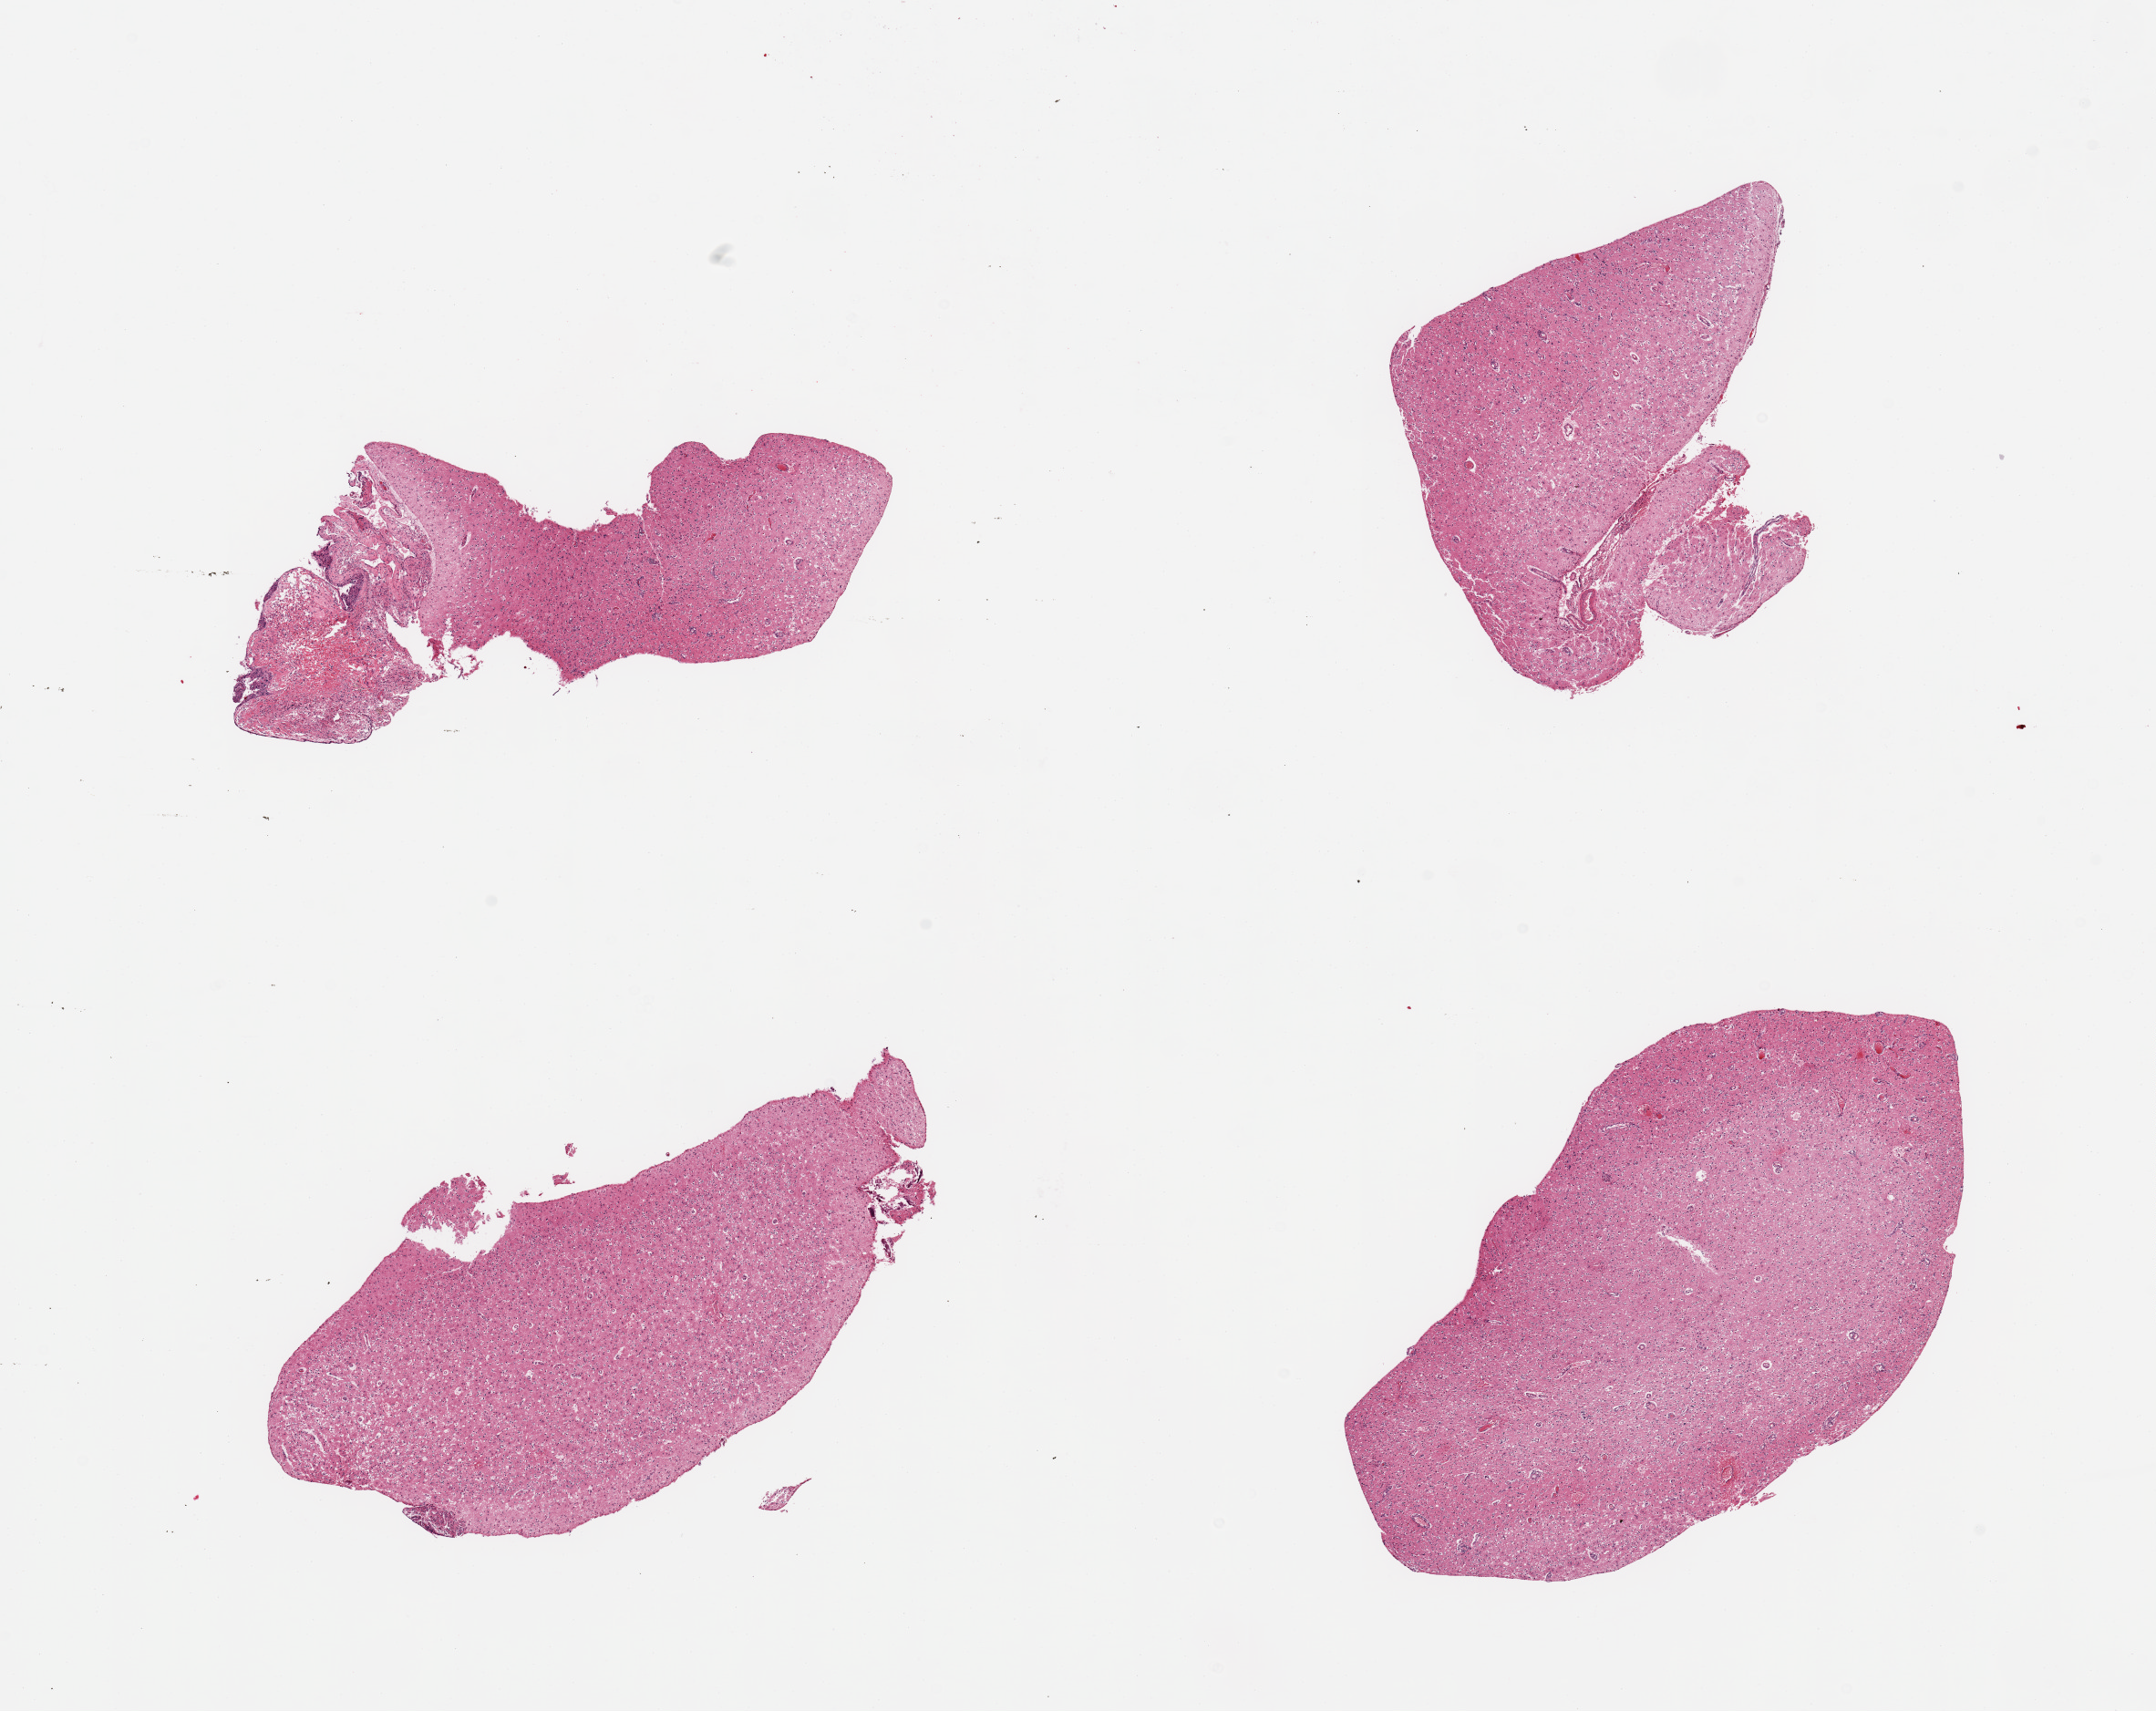
H&E whole-slide image, whole scanned area (about 18.7 x 14.8 mm, from a 20x scan) shown as a low-resolution overview; PAXgene-fixed, paraffin-embedded tissue; sampled site (target tissue): cerebral cortex; donor tissue sample. Female donor.
Reviewer comment on this tissue sample: 4 pieces, no abnormalities.